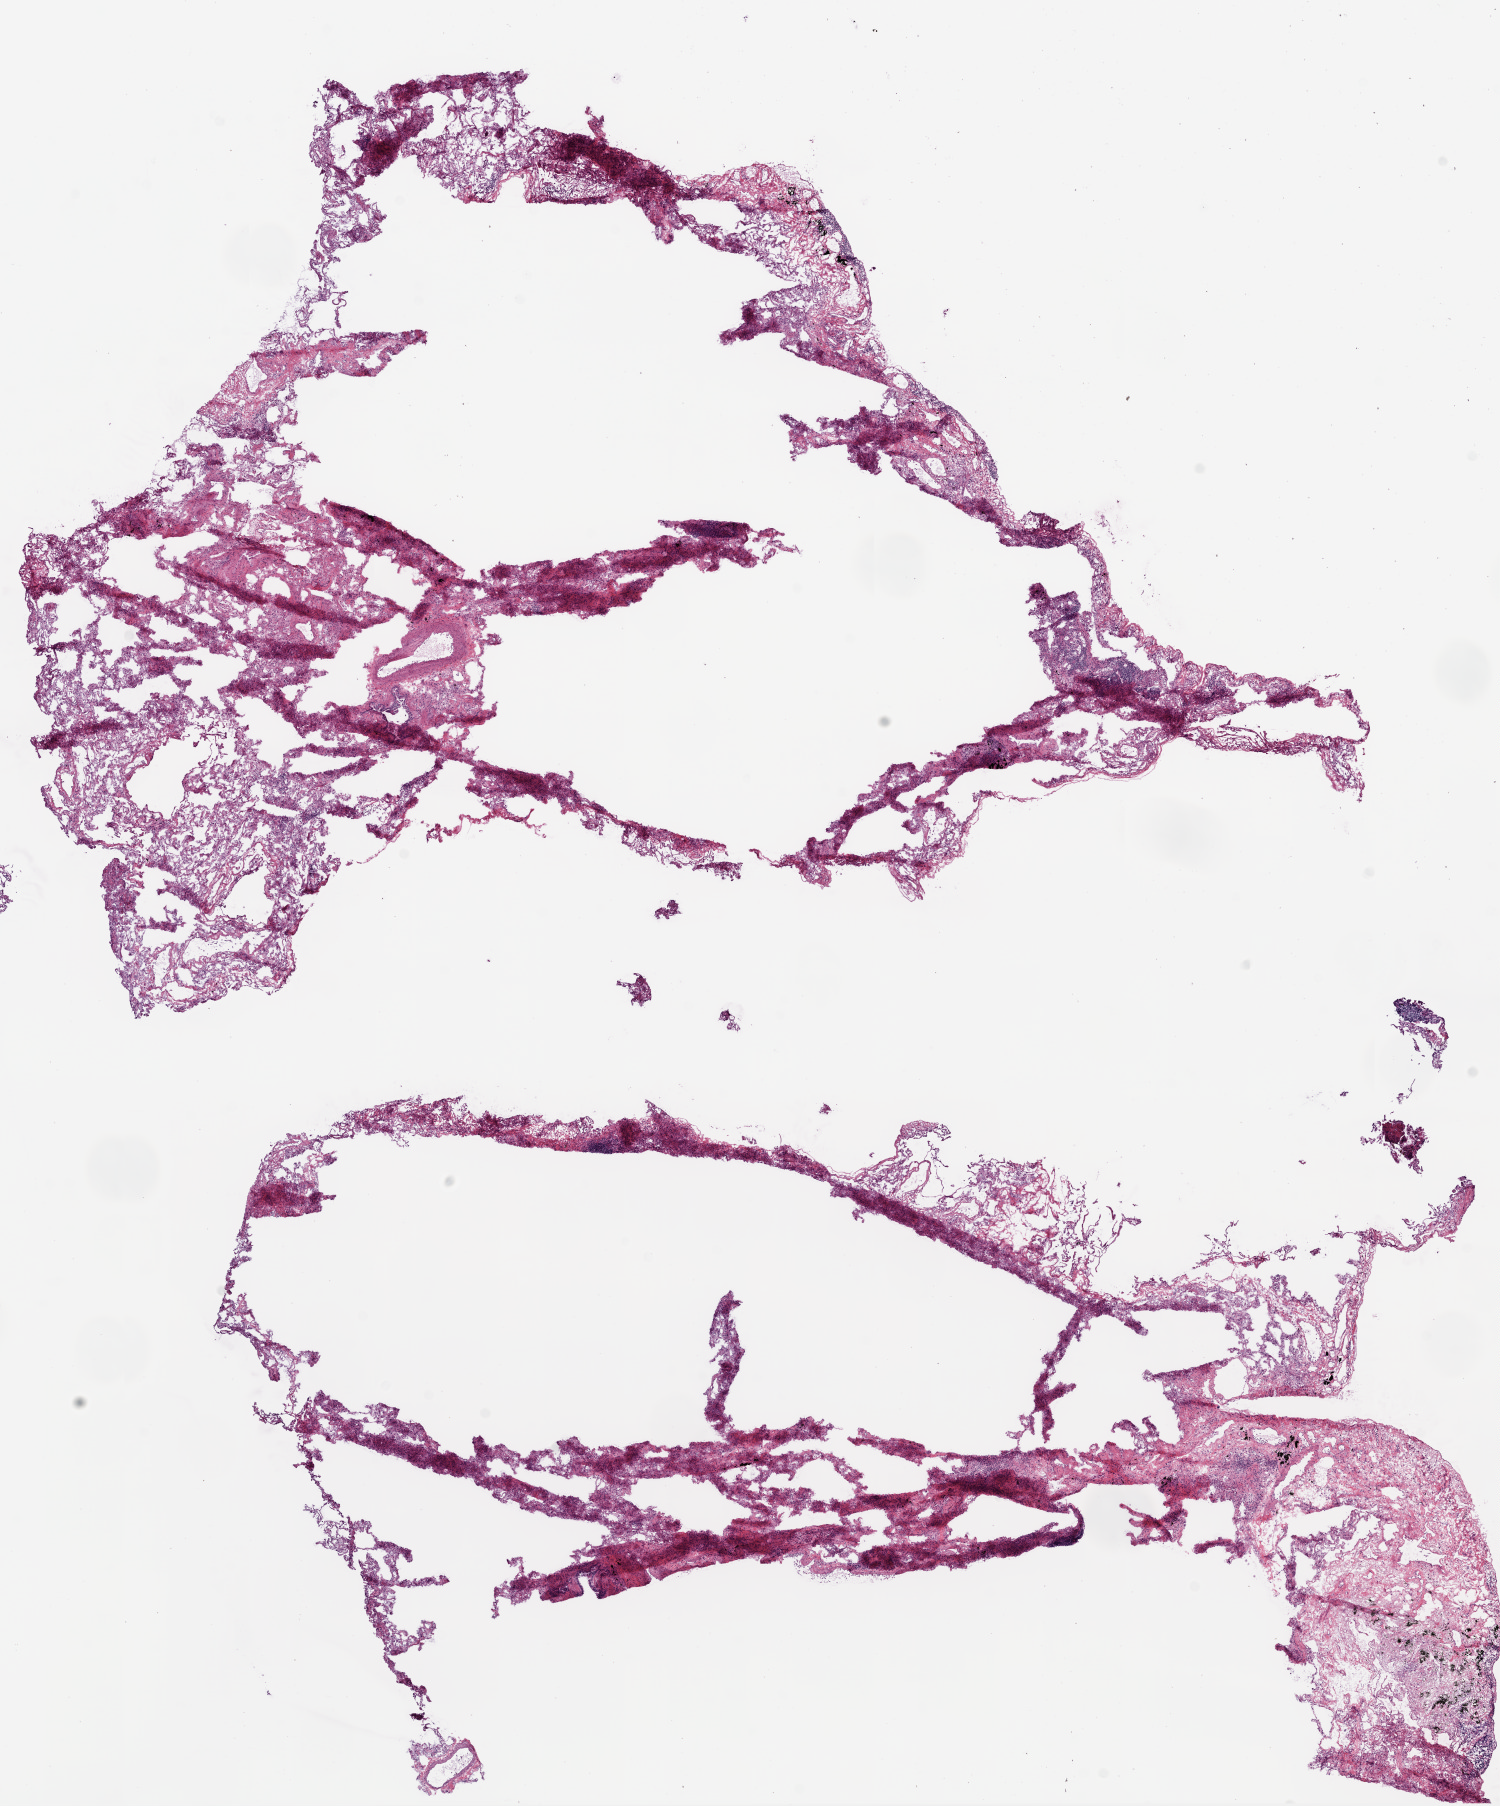
Digitized H&E tissue section (whole slide) — low-resolution overview of the scanned area, about 12.0 x 14.5 mm (from a 20x scan). Frozen section from the top of the tissue portion. Solid tissue normal (non-tumour tissue) sample from the lung. Female patient; age at initial diagnosis 76 years.
• this section: solid tissue normal (non-tumour) sample from the same patient
• patient diagnosis: Squamous cell carcinoma, NOS